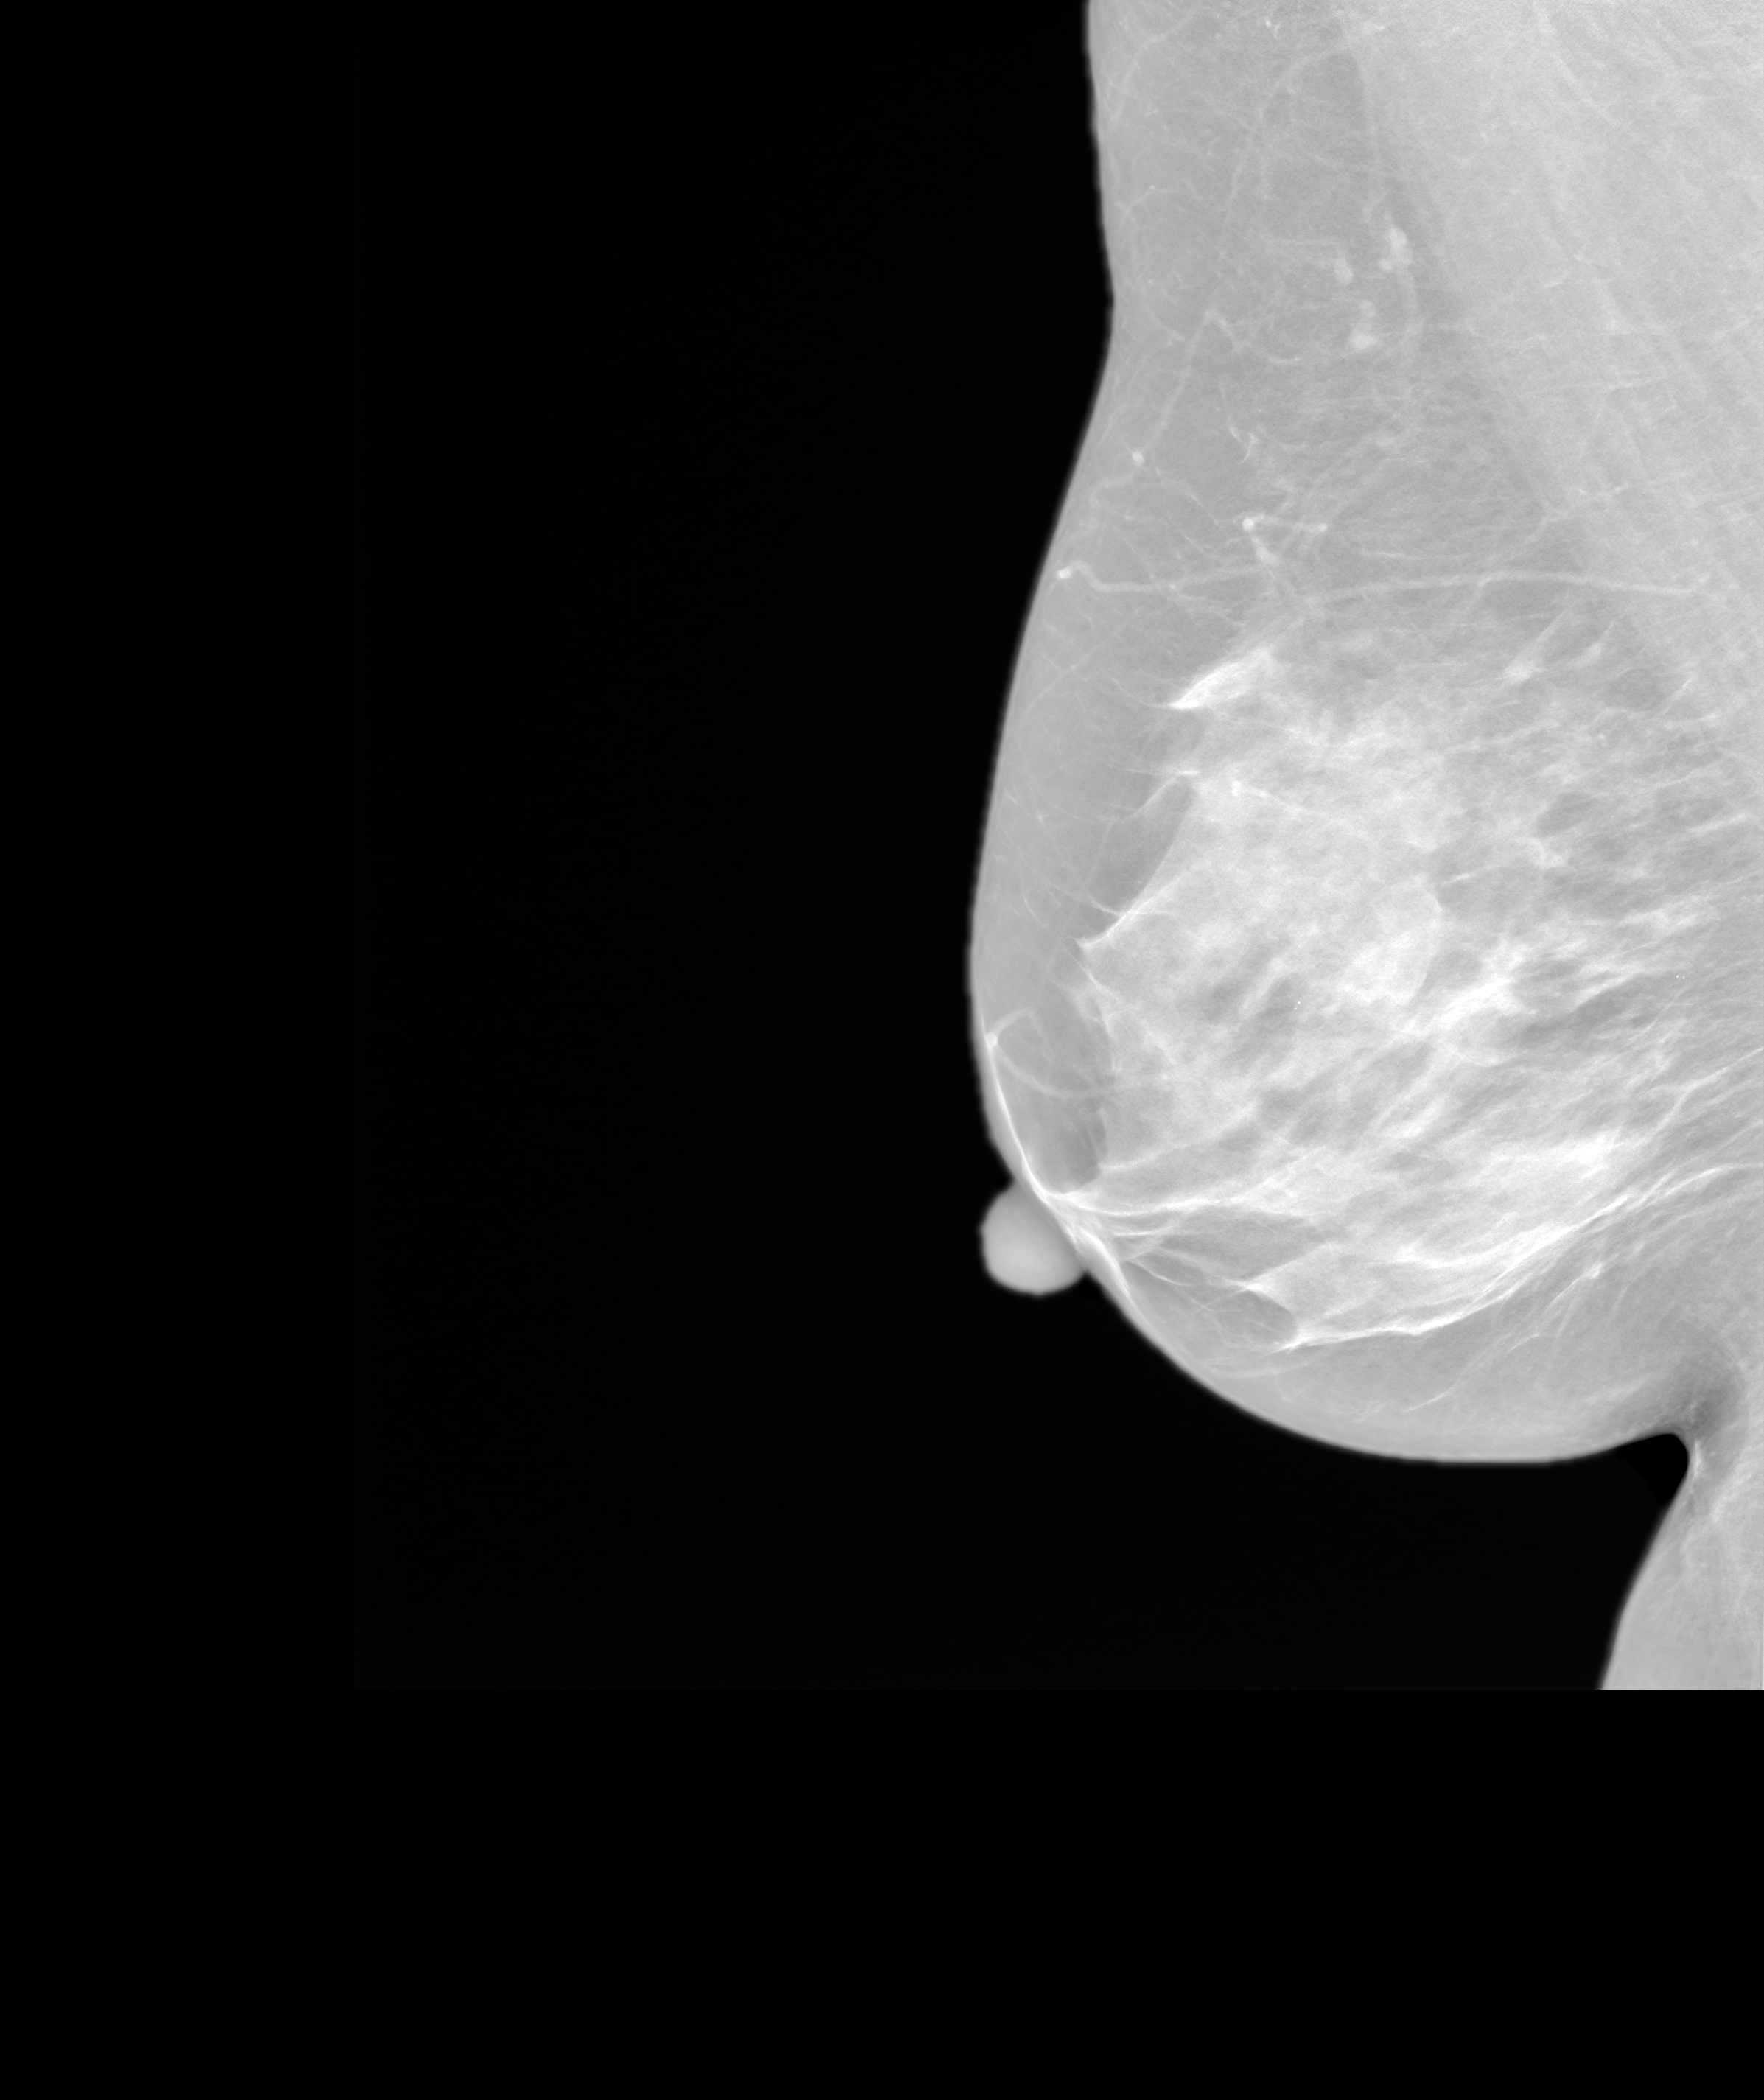
Screening examination, system: SenoIris_1SP2(440). Patient: female, 68 years.
Image type: synthesized 2-D view from tomosynthesis. Breast: right. Projection: MLO view.